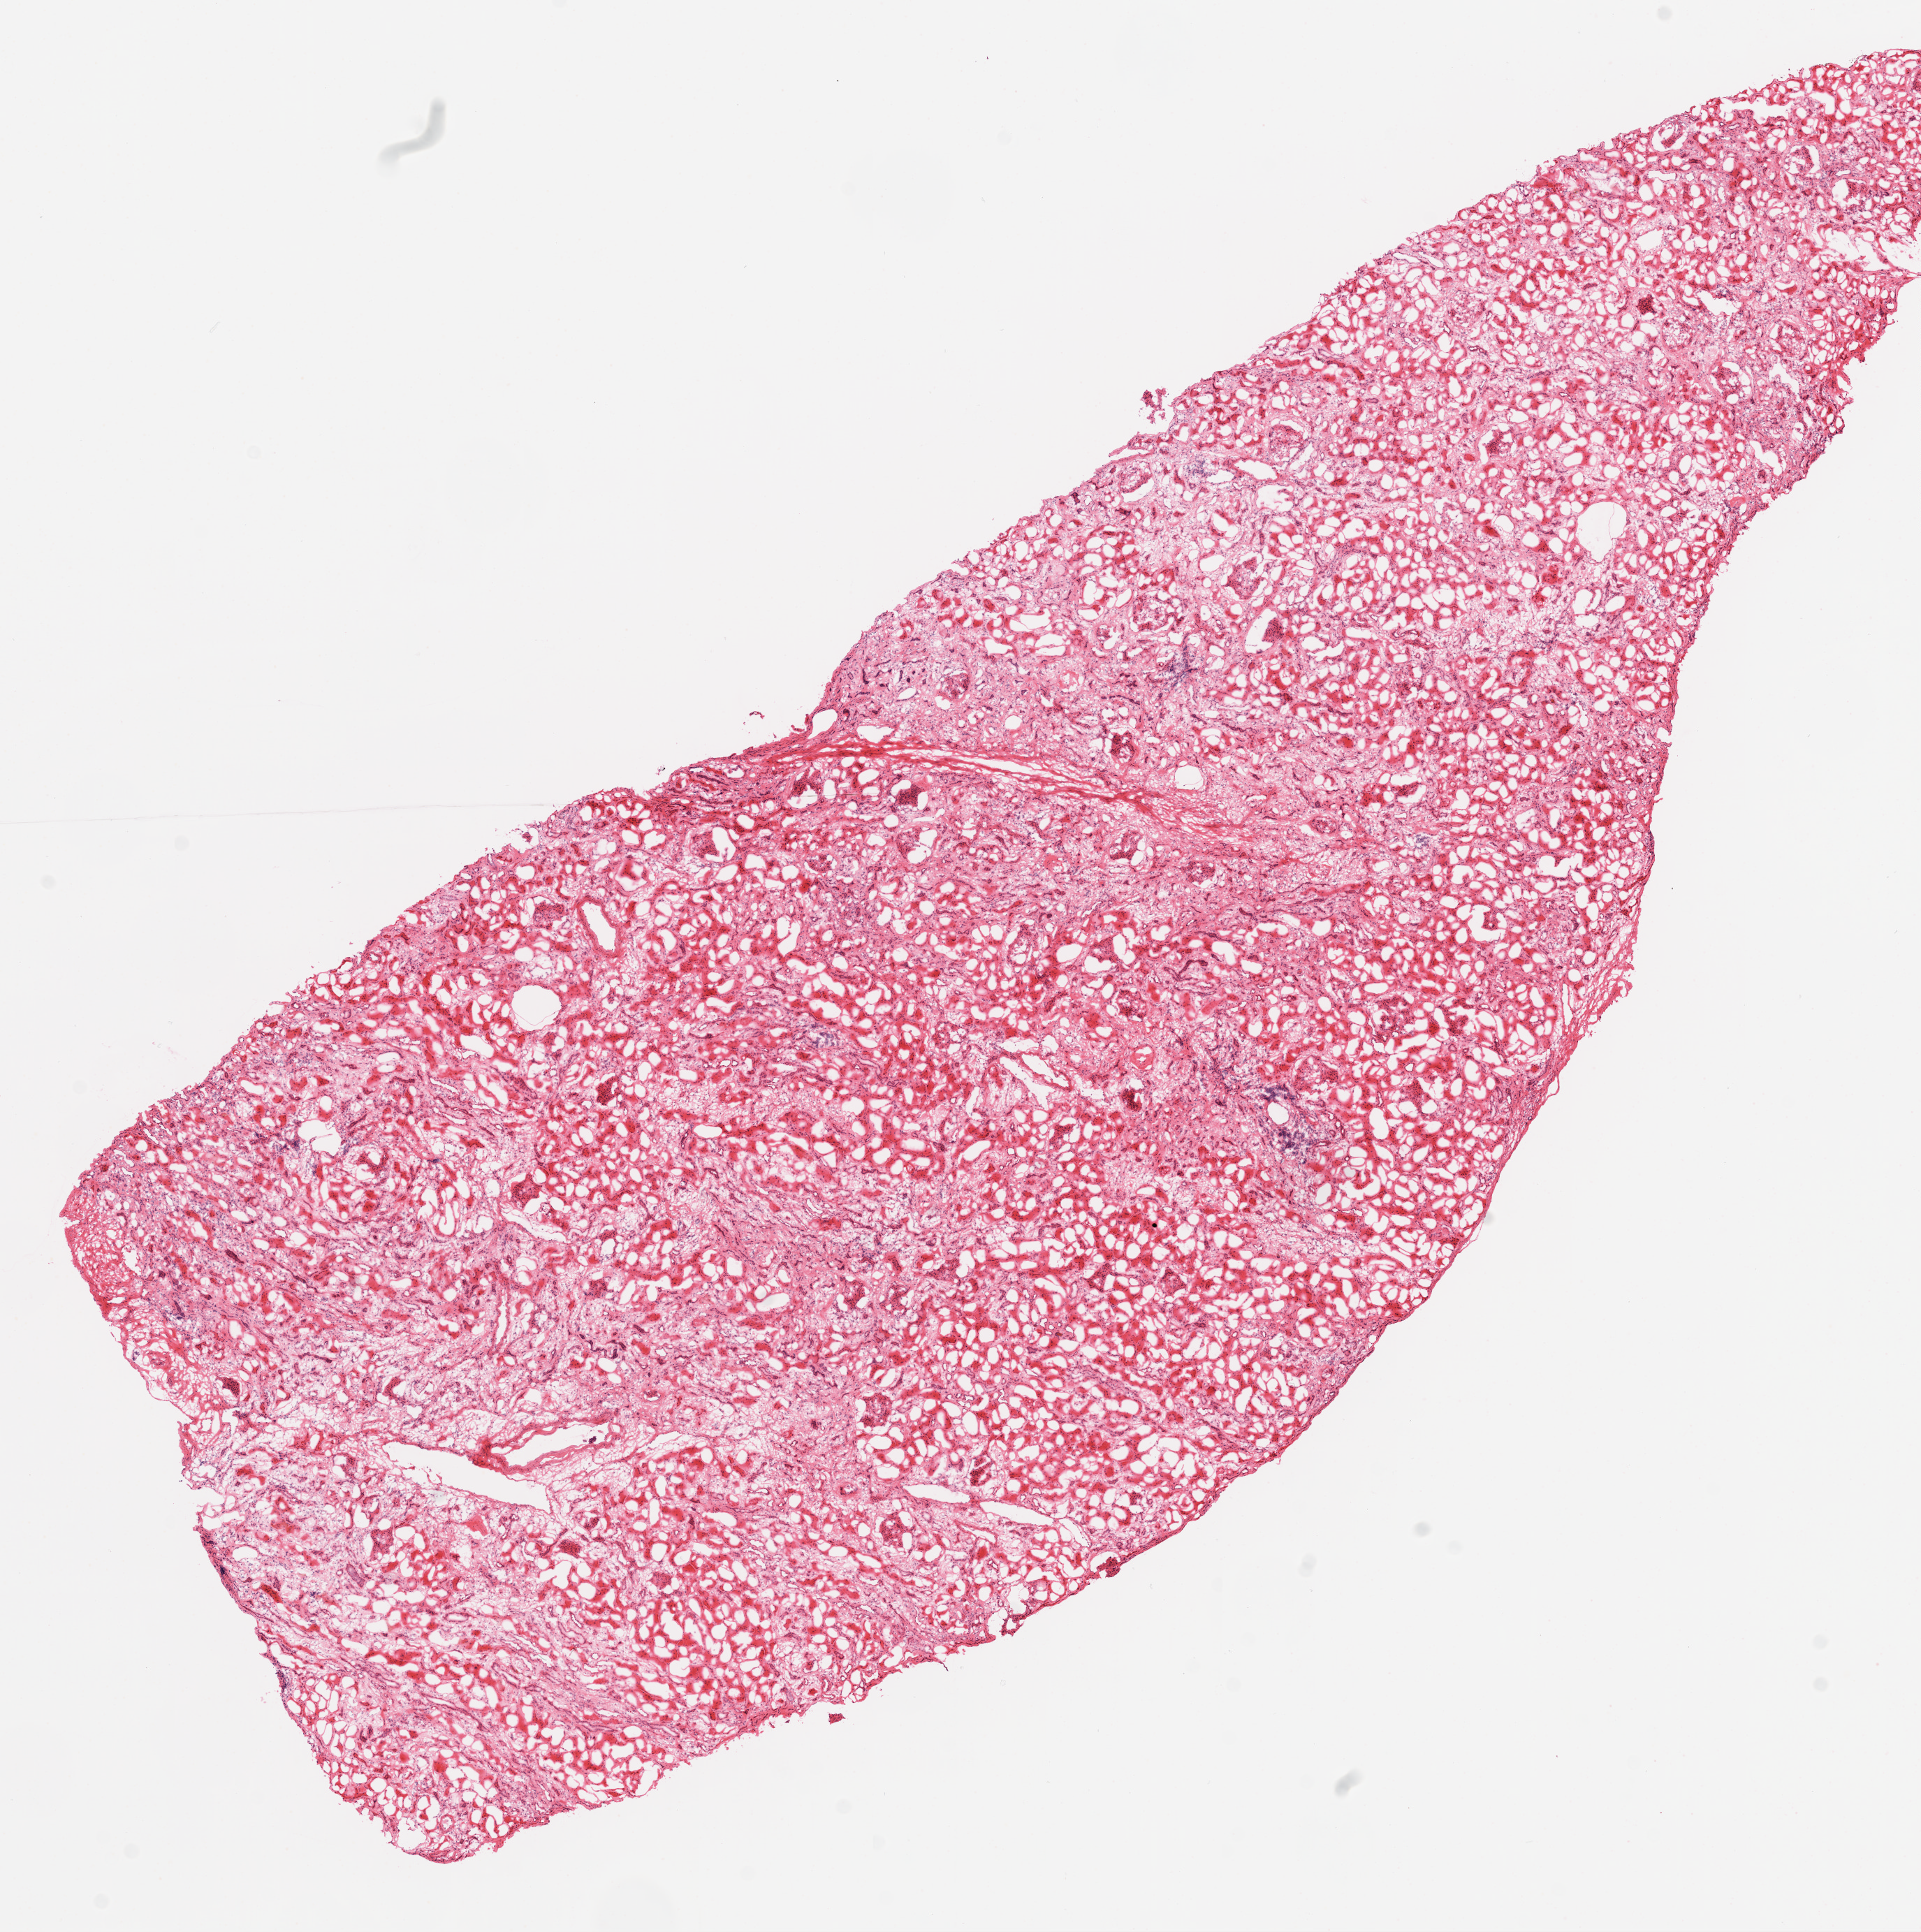
Whole-slide histology image, Hematoxylin and eosin (H&E) stained, low-resolution overview of the scanned area, about 11.0 x 11.1 mm (slide scanned at 20x). Frozen section from the top of the tissue portion. Sample: solid tissue normal (non-tumour tissue), kidney. Patient: male, age at initial diagnosis 69 years.
This section: solid tissue normal (non-tumour) sample from the same patient. Patient diagnosis: Clear cell adenocarcinoma, NOS.